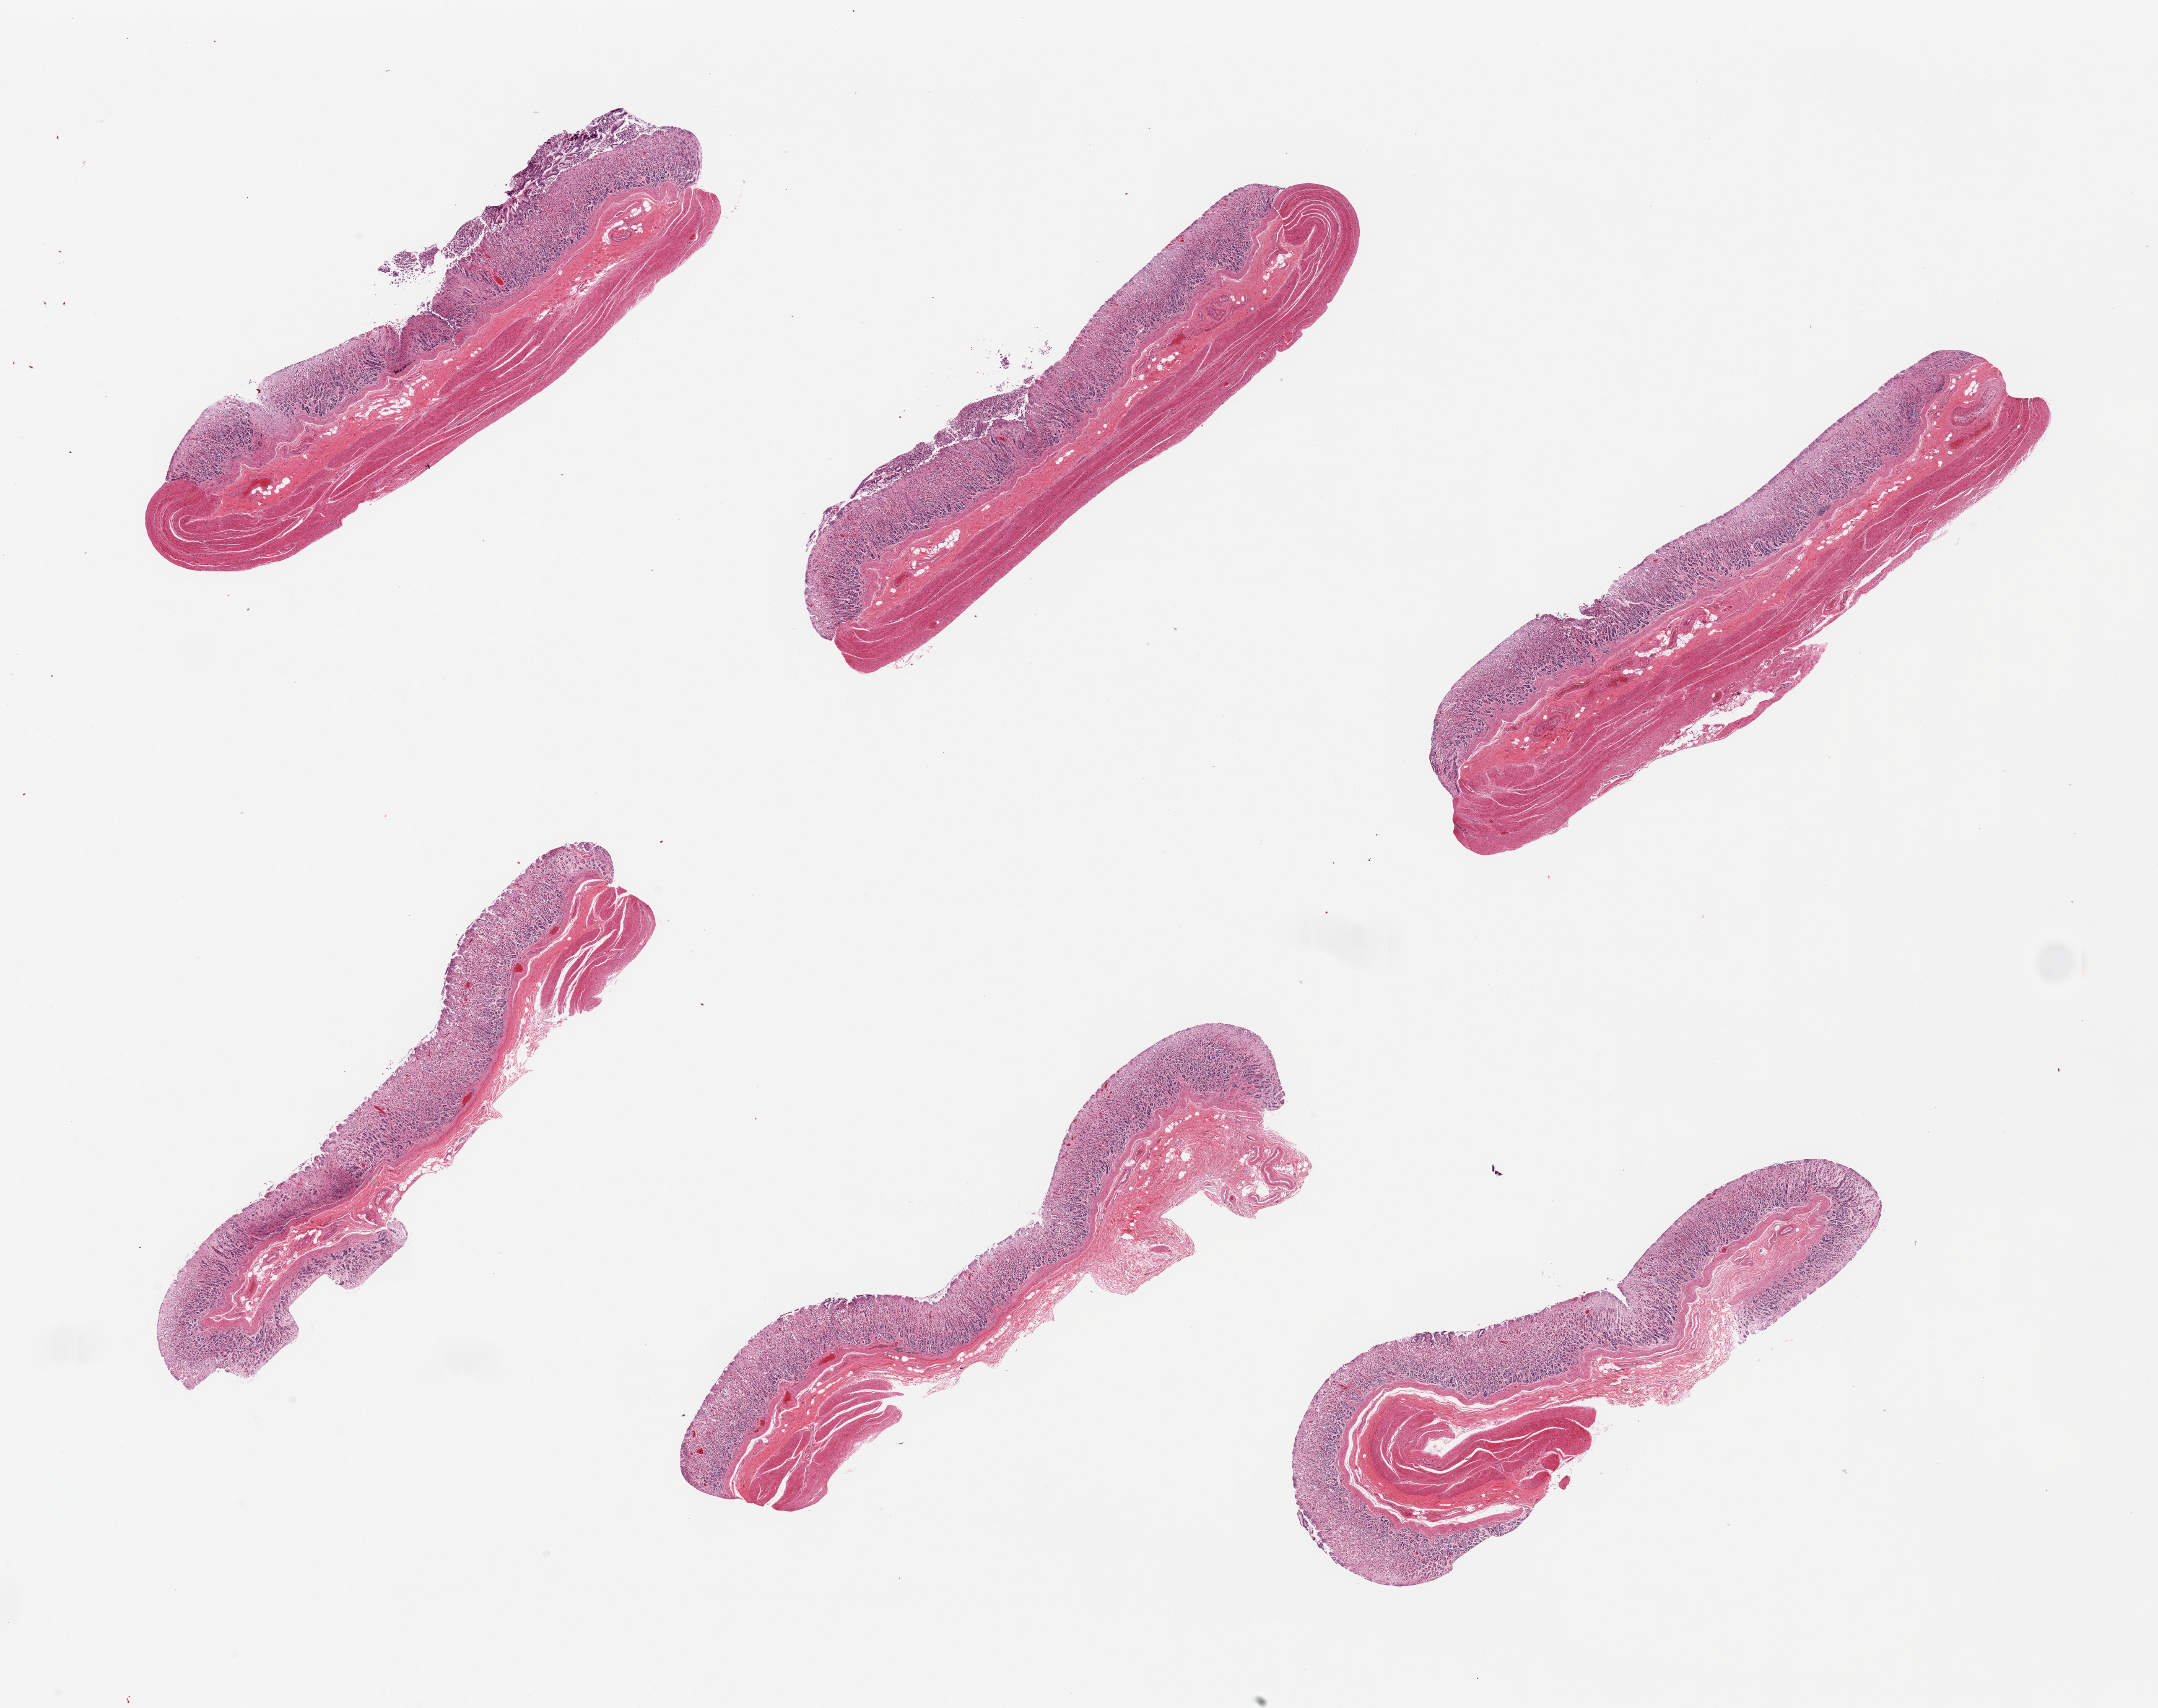
Digitized H&E-stained section, brightfield, whole scanned area (about 27.6 x 21.8 mm) shown as a low-resolution overview; PAXgene-fixed, paraffin-embedded tissue; section of stomach (target tissue); donor tissue sample. Donor: female.
* review note (as recorded): 6 pieces, mucosa up to 1mm thick;30-90 % of thickness but badly autolyzed, in some foci a 3